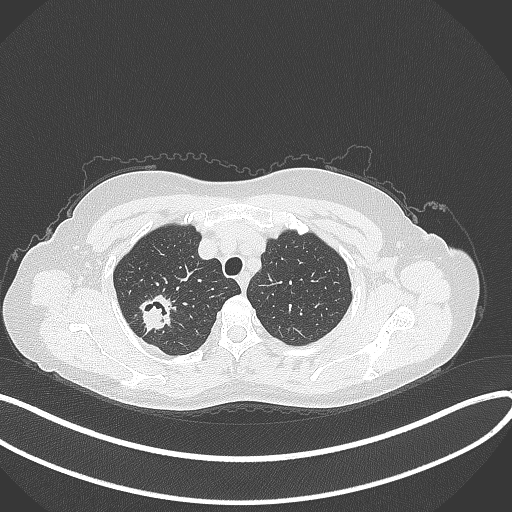
Chest CT, one axial slice; slice 301 of 337 in the series (ordered by position); reconstruction kernel B70f; 120 kVp; lung window (W 1500 / L -600 HU); 512 × 512 image matrix. Patient: female, 50 years. From the clinical record (not read from this slice): clinical TNM (as recorded): T1c N0 M0.
Annotated regions visible in this slice (rectangle marked by the reading radiologist):
- lung tumour (recorded histology: adenocarcinoma): bounding box (x1, y1, x2, y2) in pixels: (135, 293, 178, 335)